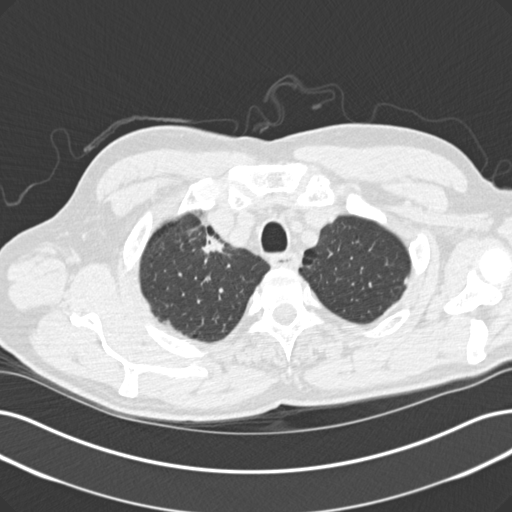
Low-dose screening chest CT, one axial slice. Slice 128 of 152 in the series (ordered by position). Lung window (W 1500 / L -600 HU). 2 mm slice thickness. 512 × 512 image matrix.
Annotated regions visible in this slice (outlined manually by an expert reader):
- lesion 1 (tumor, upper lobe of right lung): bounding box <202,234,224,259> (left, top, right, bottom; pixels)